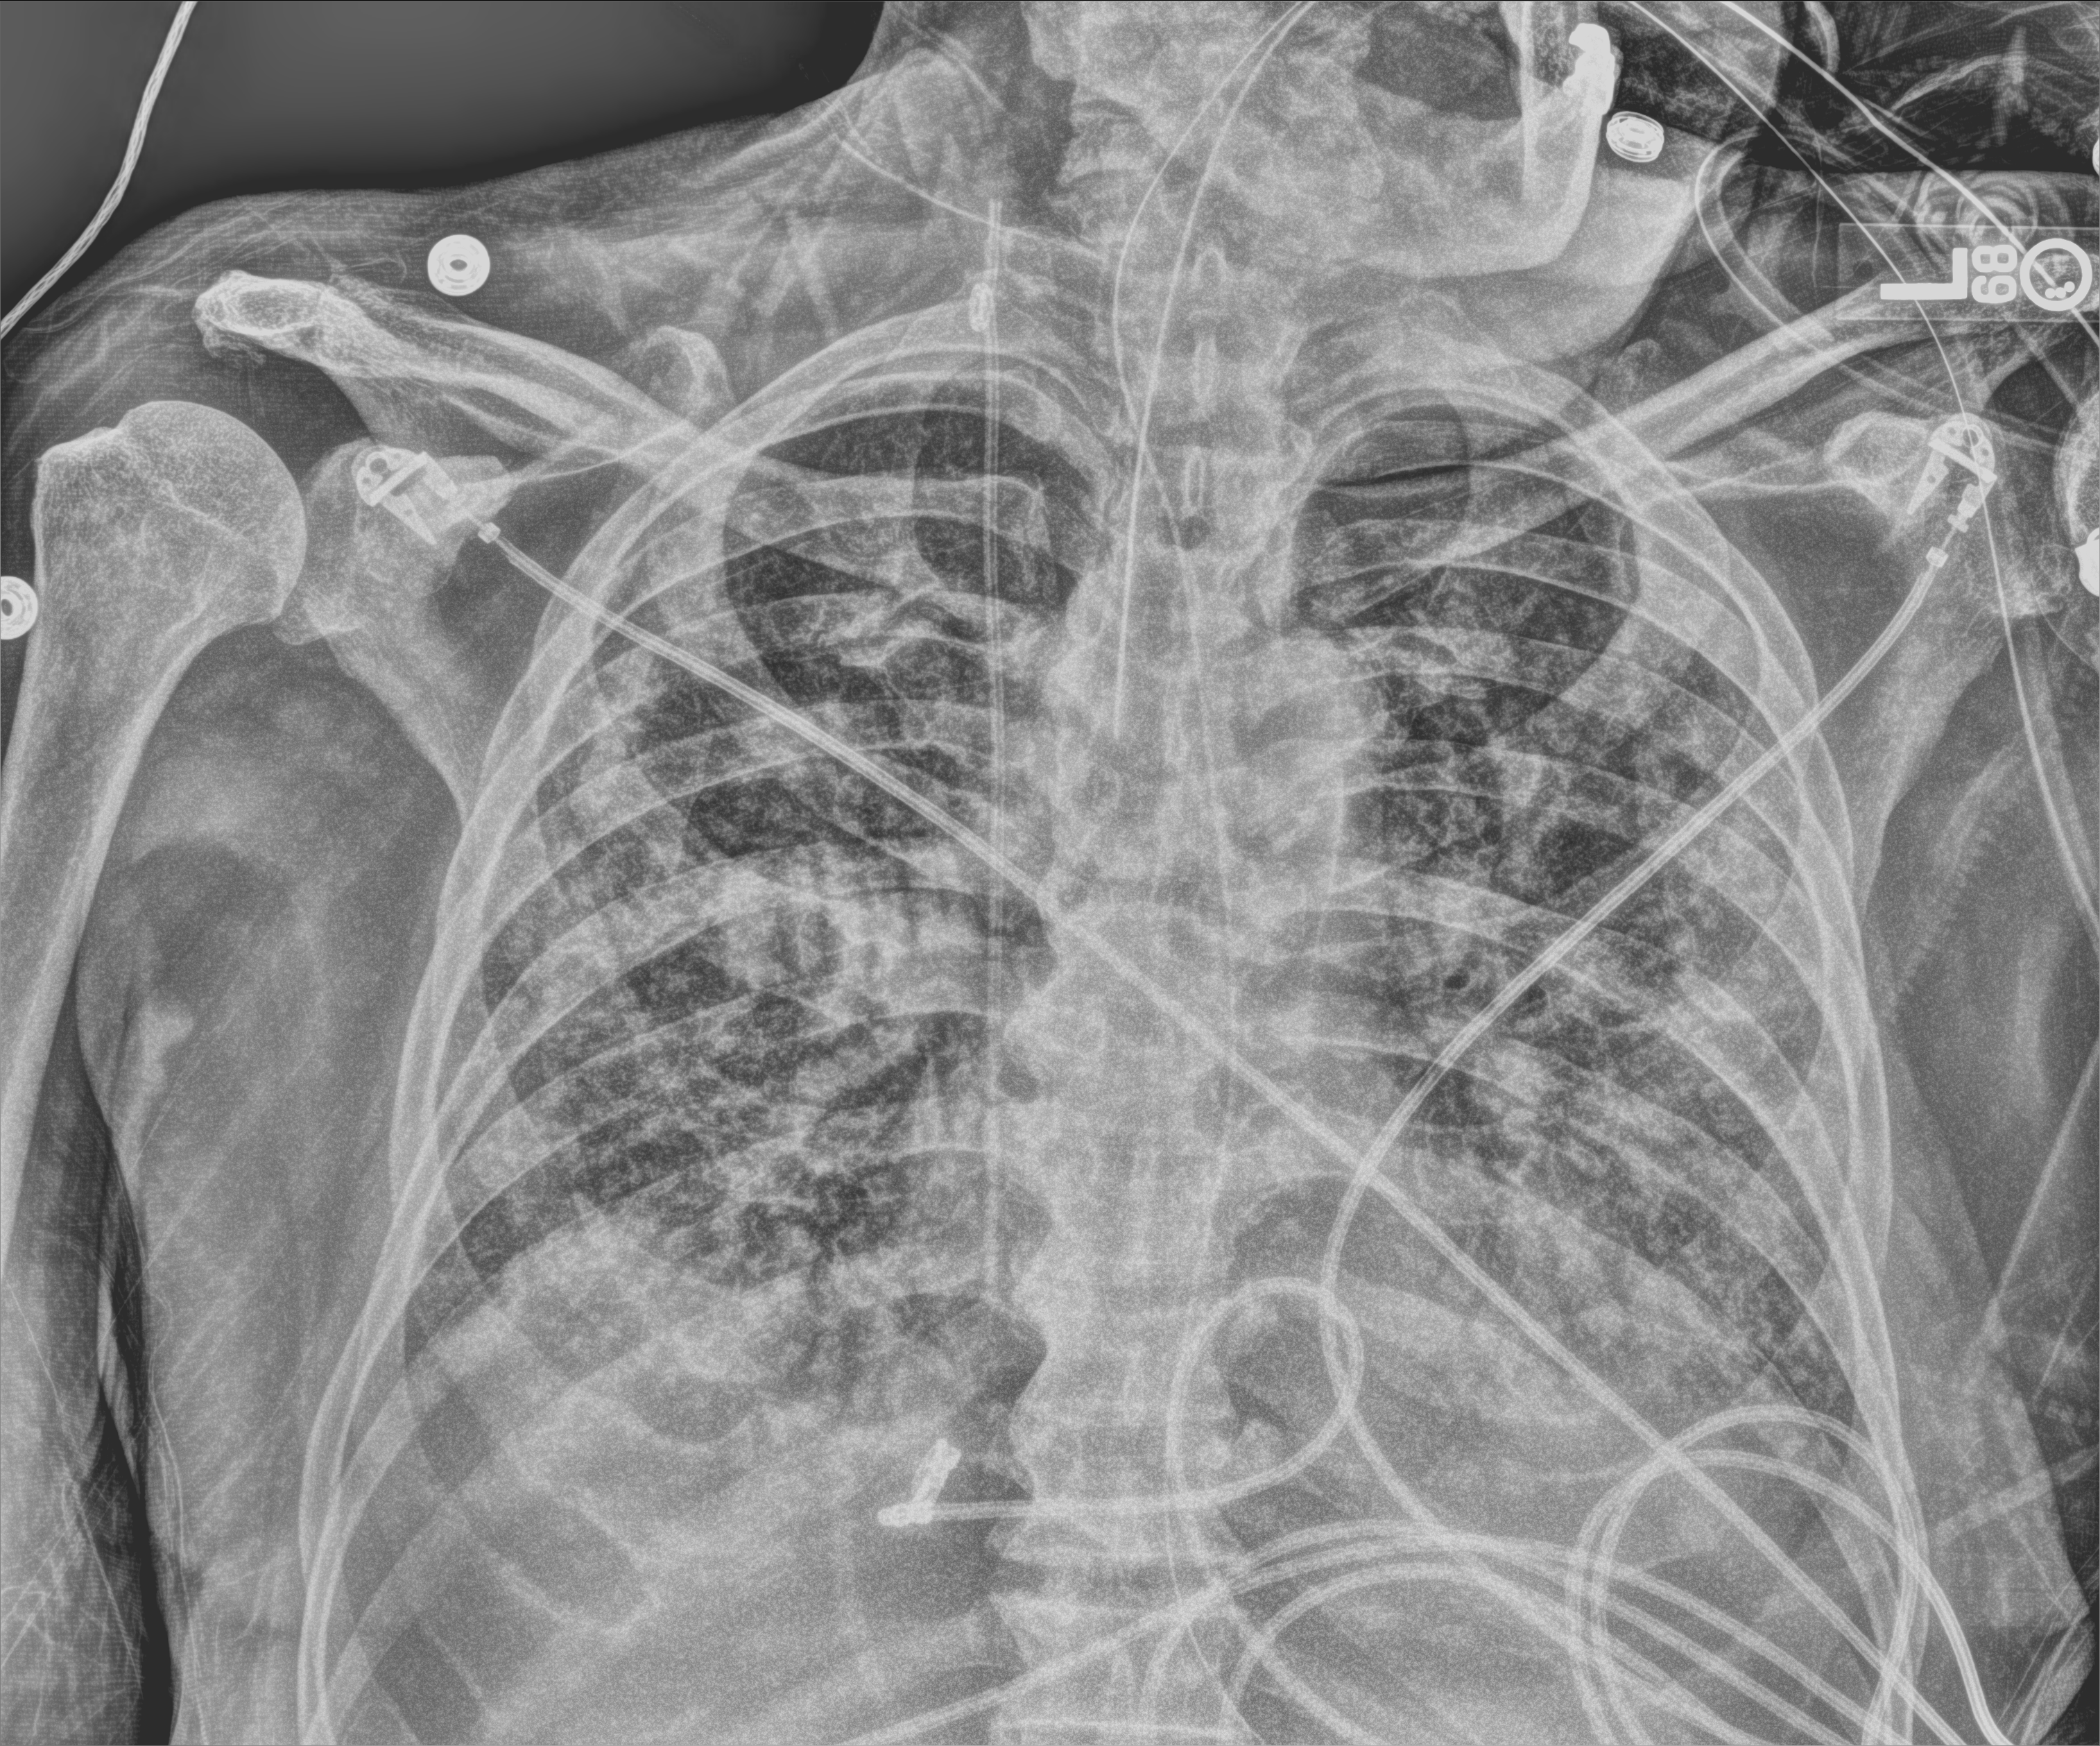
Portable chest radiograph; anteroposterior (AP) projection. Patient hospitalised with COVID-19; male, aged 75–90 years.
Hospital-stay facts (about this admission, not read from this image; timing relative to this image not recorded): hypertension (admission record): yes.